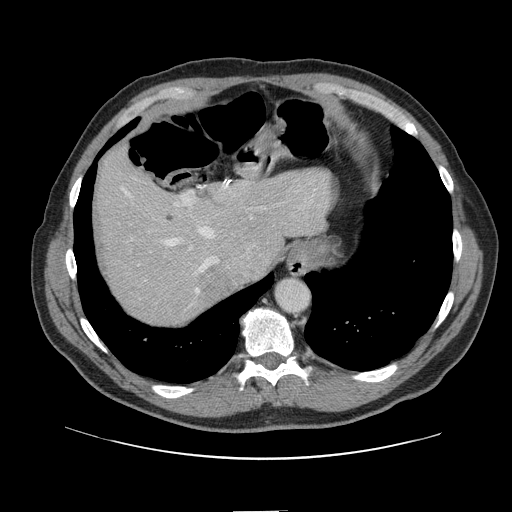
Contrast-enhanced abdominal CT, one axial slice. Position 115 of 161 along the scan axis. 120 kVp. Intravenous contrast given. Soft-tissue window (W 400 / L 40 HU). 2.5 mm slice thickness. 512 × 512 image matrix, field of view 412 × 412 mm. Male patient, age 66 years. Case-level facts recorded for this patient, not image findings: diagnosis: colorectal cancer liver metastases, imaged before liver resection; multiple liver metastases: no; largest metastasis: 3.5 cm; chemotherapy before resection: yes.
Outlined on this slice (expert manual segmentation):
- hepatic veins: bounding box <121,186,253,295> (left, top, right, bottom; pixels)
- liver: <98,150,326,323>
- planned liver remnant (the part of the liver to remain after resection): <98,152,327,303>
- portal vein (with intrahepatic branches): <175,192,252,209>
- liver metastasis: <192,264,234,297>